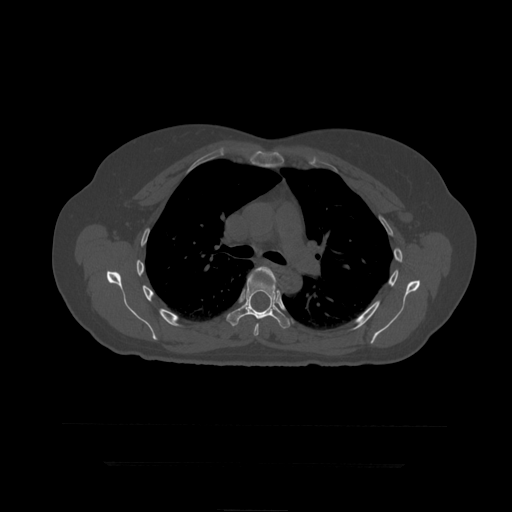
CT including the spine, one axial slice; slice 307 of 399 in the series (ordered by position); reconstruction kernel STANDARD; 120 kVp; bone window (W 1800 / L 400 HU); 1.25 mm slice thickness; 512 × 512 image matrix, field of view 450 × 450 mm. Patient age 41 years. Case-level facts recorded for this patient, not image findings: primary cancer: breast.
Structures marked on this image (semi-automatically segmented with operator editing):
- T6 vertebra: bounding box (x1, y1, x2, y2) in pixels: (254, 267, 276, 336)
- T7 vertebra: (227, 272, 291, 329)